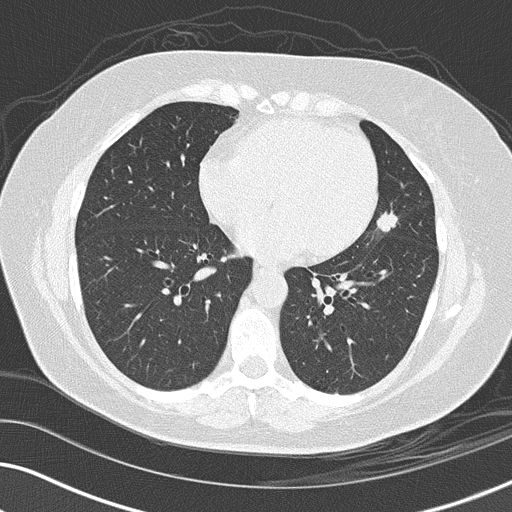
Chest CT (low-dose screening protocol), one axial image; third annual screen; lung window (W 1500 / L -600 HU); 2 mm slice thickness; lung (sharp) reconstruction kernel (B50f); slice 85 of 152 in the series; 512 × 512 image matrix. Female participant, aged 56 years at enrolment.
- Lesion marked by an expert reader, bounding box (x1, y1, x2, y2) in pixels: (356, 199, 411, 248).
- Screening reader's record for this exam (one nodule recorded; not confirmed to be the boxed lesion): non-calcified nodule or mass ≥4 mm, lingula, 14 × 14 mm, spiculated (stellate) margins, soft tissue attenuation, pre-existing on the prior screen: yes; interval growth: yes.
- Participant outcome: lung cancer diagnosed 86 days after this screen — adenocarcinoma, NOS, left upper lobe, poorly differentiated (G3), stage IIIA (AJCC 6th edition), 15 mm at pathology.